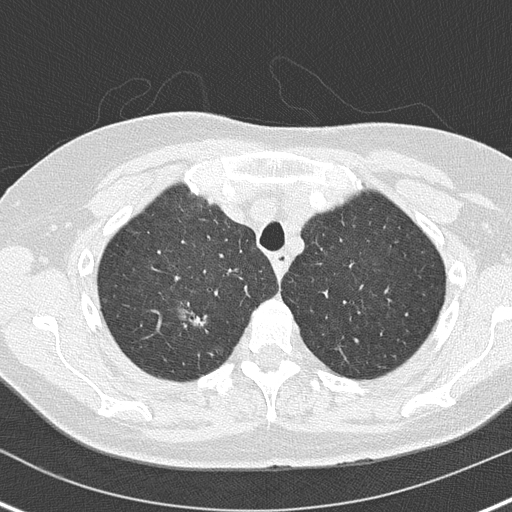
Low-dose screening chest CT, axial slice; baseline screening round; lung window (W 1500 / L -600 HU); 2 mm slice thickness; 512 × 512 image matrix, field of view 300 × 300 mm. Female participant, aged 61 years at enrolment.
Lesion marked by an expert reader, box from (x=182, y=305) to (x=217, y=335) px. Reader record for this screening exam (exam-level; its link to the box is not recorded): non-calcified nodule or mass ≥4 mm, right upper lobe, 8 × 5 mm, smooth margins, soft tissue attenuation. Official screen result: positive, change unspecified: nodule(s) >= 4 mm or enlarging nodule(s), mass(es), or other non-specific abnormalities suspicious for lung cancer. Later outcome: lung cancer diagnosed 438 days after this screen (after the second annual screen) — adenocarcinoma, NOS, right upper lobe, moderately differentiated (G2), stage IA (AJCC 6th edition), 20 mm at pathology.